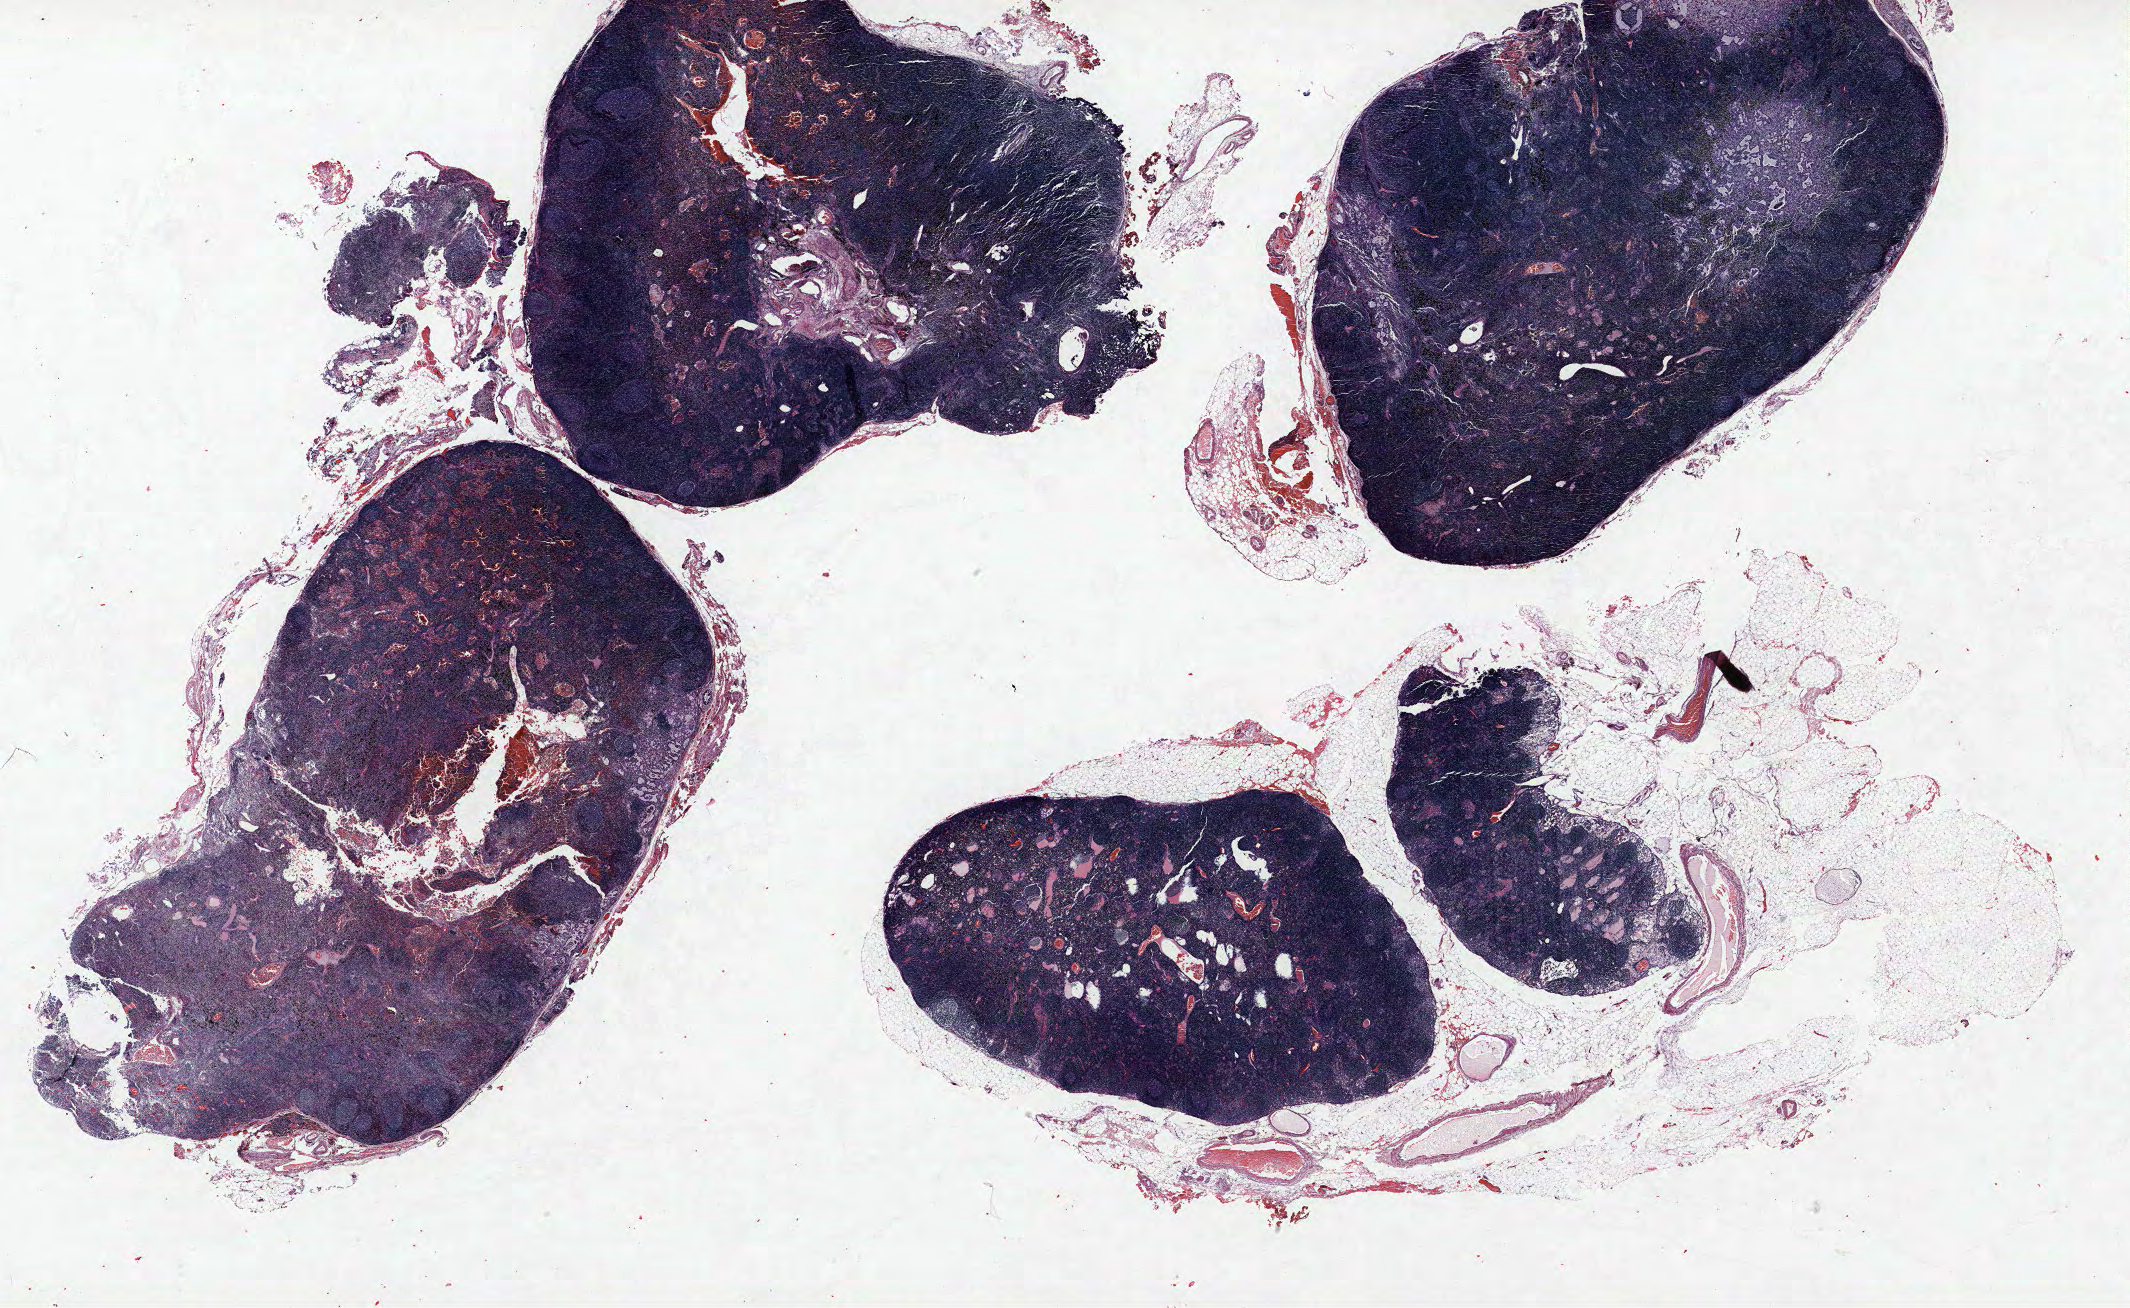
Whole-slide histology image, H&E-stained, shown as a low-resolution overview of the whole scanned area (about 34.1 x 20.9 mm, acquisition: 40x scan); formalin-fixed paraffin-embedded (FFPE) section; lung tissue. Female, age 73 at enrolment. Grade: well differentiated (G1).
• participant's lung-cancer diagnosis: Mucinous adenocarcinoma
• primary tumour location (clinical record): right lower lobe
• tumour size (pathology): 85 mm
• stage (AJCC 6th edition): IV